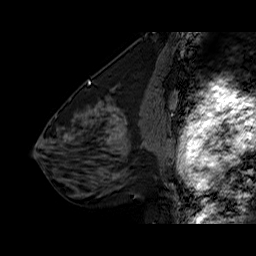
Breast MRI (dynamic contrast-enhanced), one sagittal slice. Position 30 of 60 along the scan axis. Dynamic contrast-enhanced series, time point 2 of 6 at this slice position (early post-contrast). 1.5 T. TE 6.3 ms, TR 32.5 ms. 256 × 256 image matrix, field of view 200 × 200 mm. Female patient. Case-level facts recorded for this patient, not image findings: setting: breast cancer imaged before/during neoadjuvant chemotherapy; receptor status: triple-negative.
Structures marked on this image (semi-automatically segmented with operator editing):
- analysis volume of interest (the breast-tissue region the enhancement analysis was run in; not a lesion): bounding box <108,126,154,177> (left, top, right, bottom; pixels)
- tumour enhancement mask (voxels above the 100 % enhancement threshold inside the analysis volume of interest): <108,129,124,143>